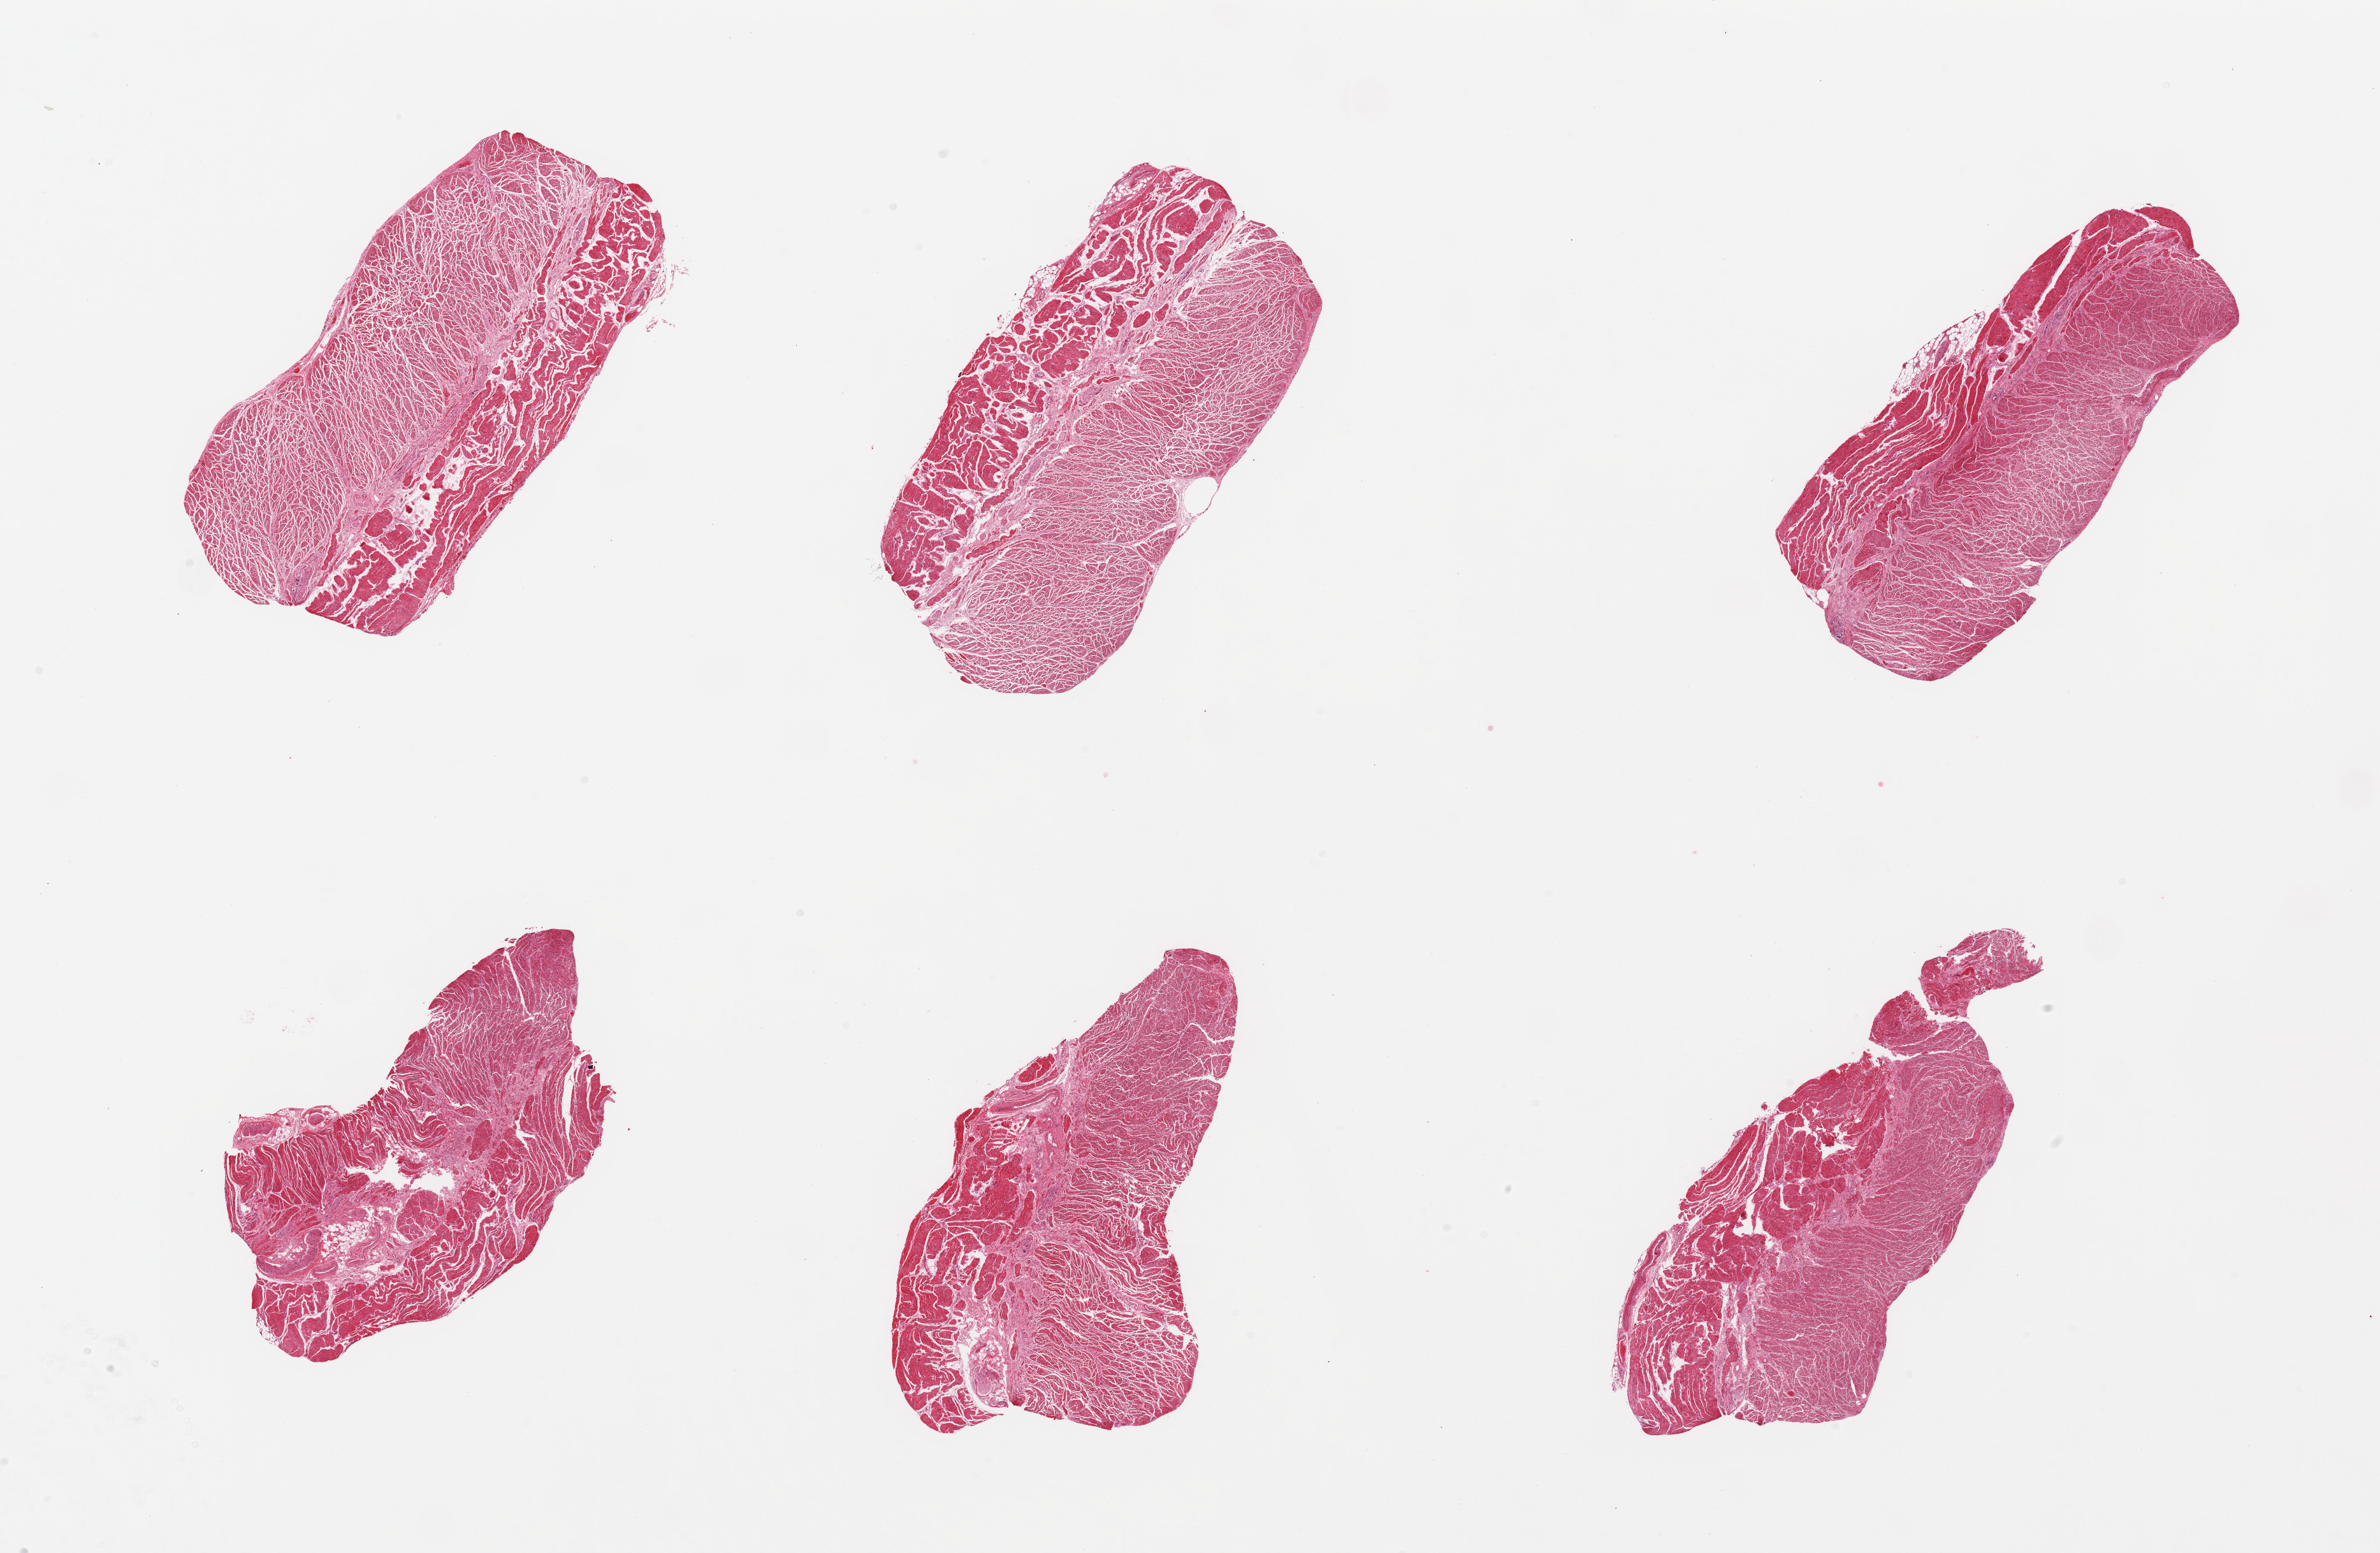
Whole-slide image, haematoxylin and eosin stain — low-resolution overview of the scanned area, about 29.5 x 19.3 mm (slide scanned at 20x), PAXgene-fixed, paraffin-embedded tissue, target tissue: esophageal muscle, tissue donor sample. Male donor.
Review note (as recorded): 6 pieces; well dissected muscularis.